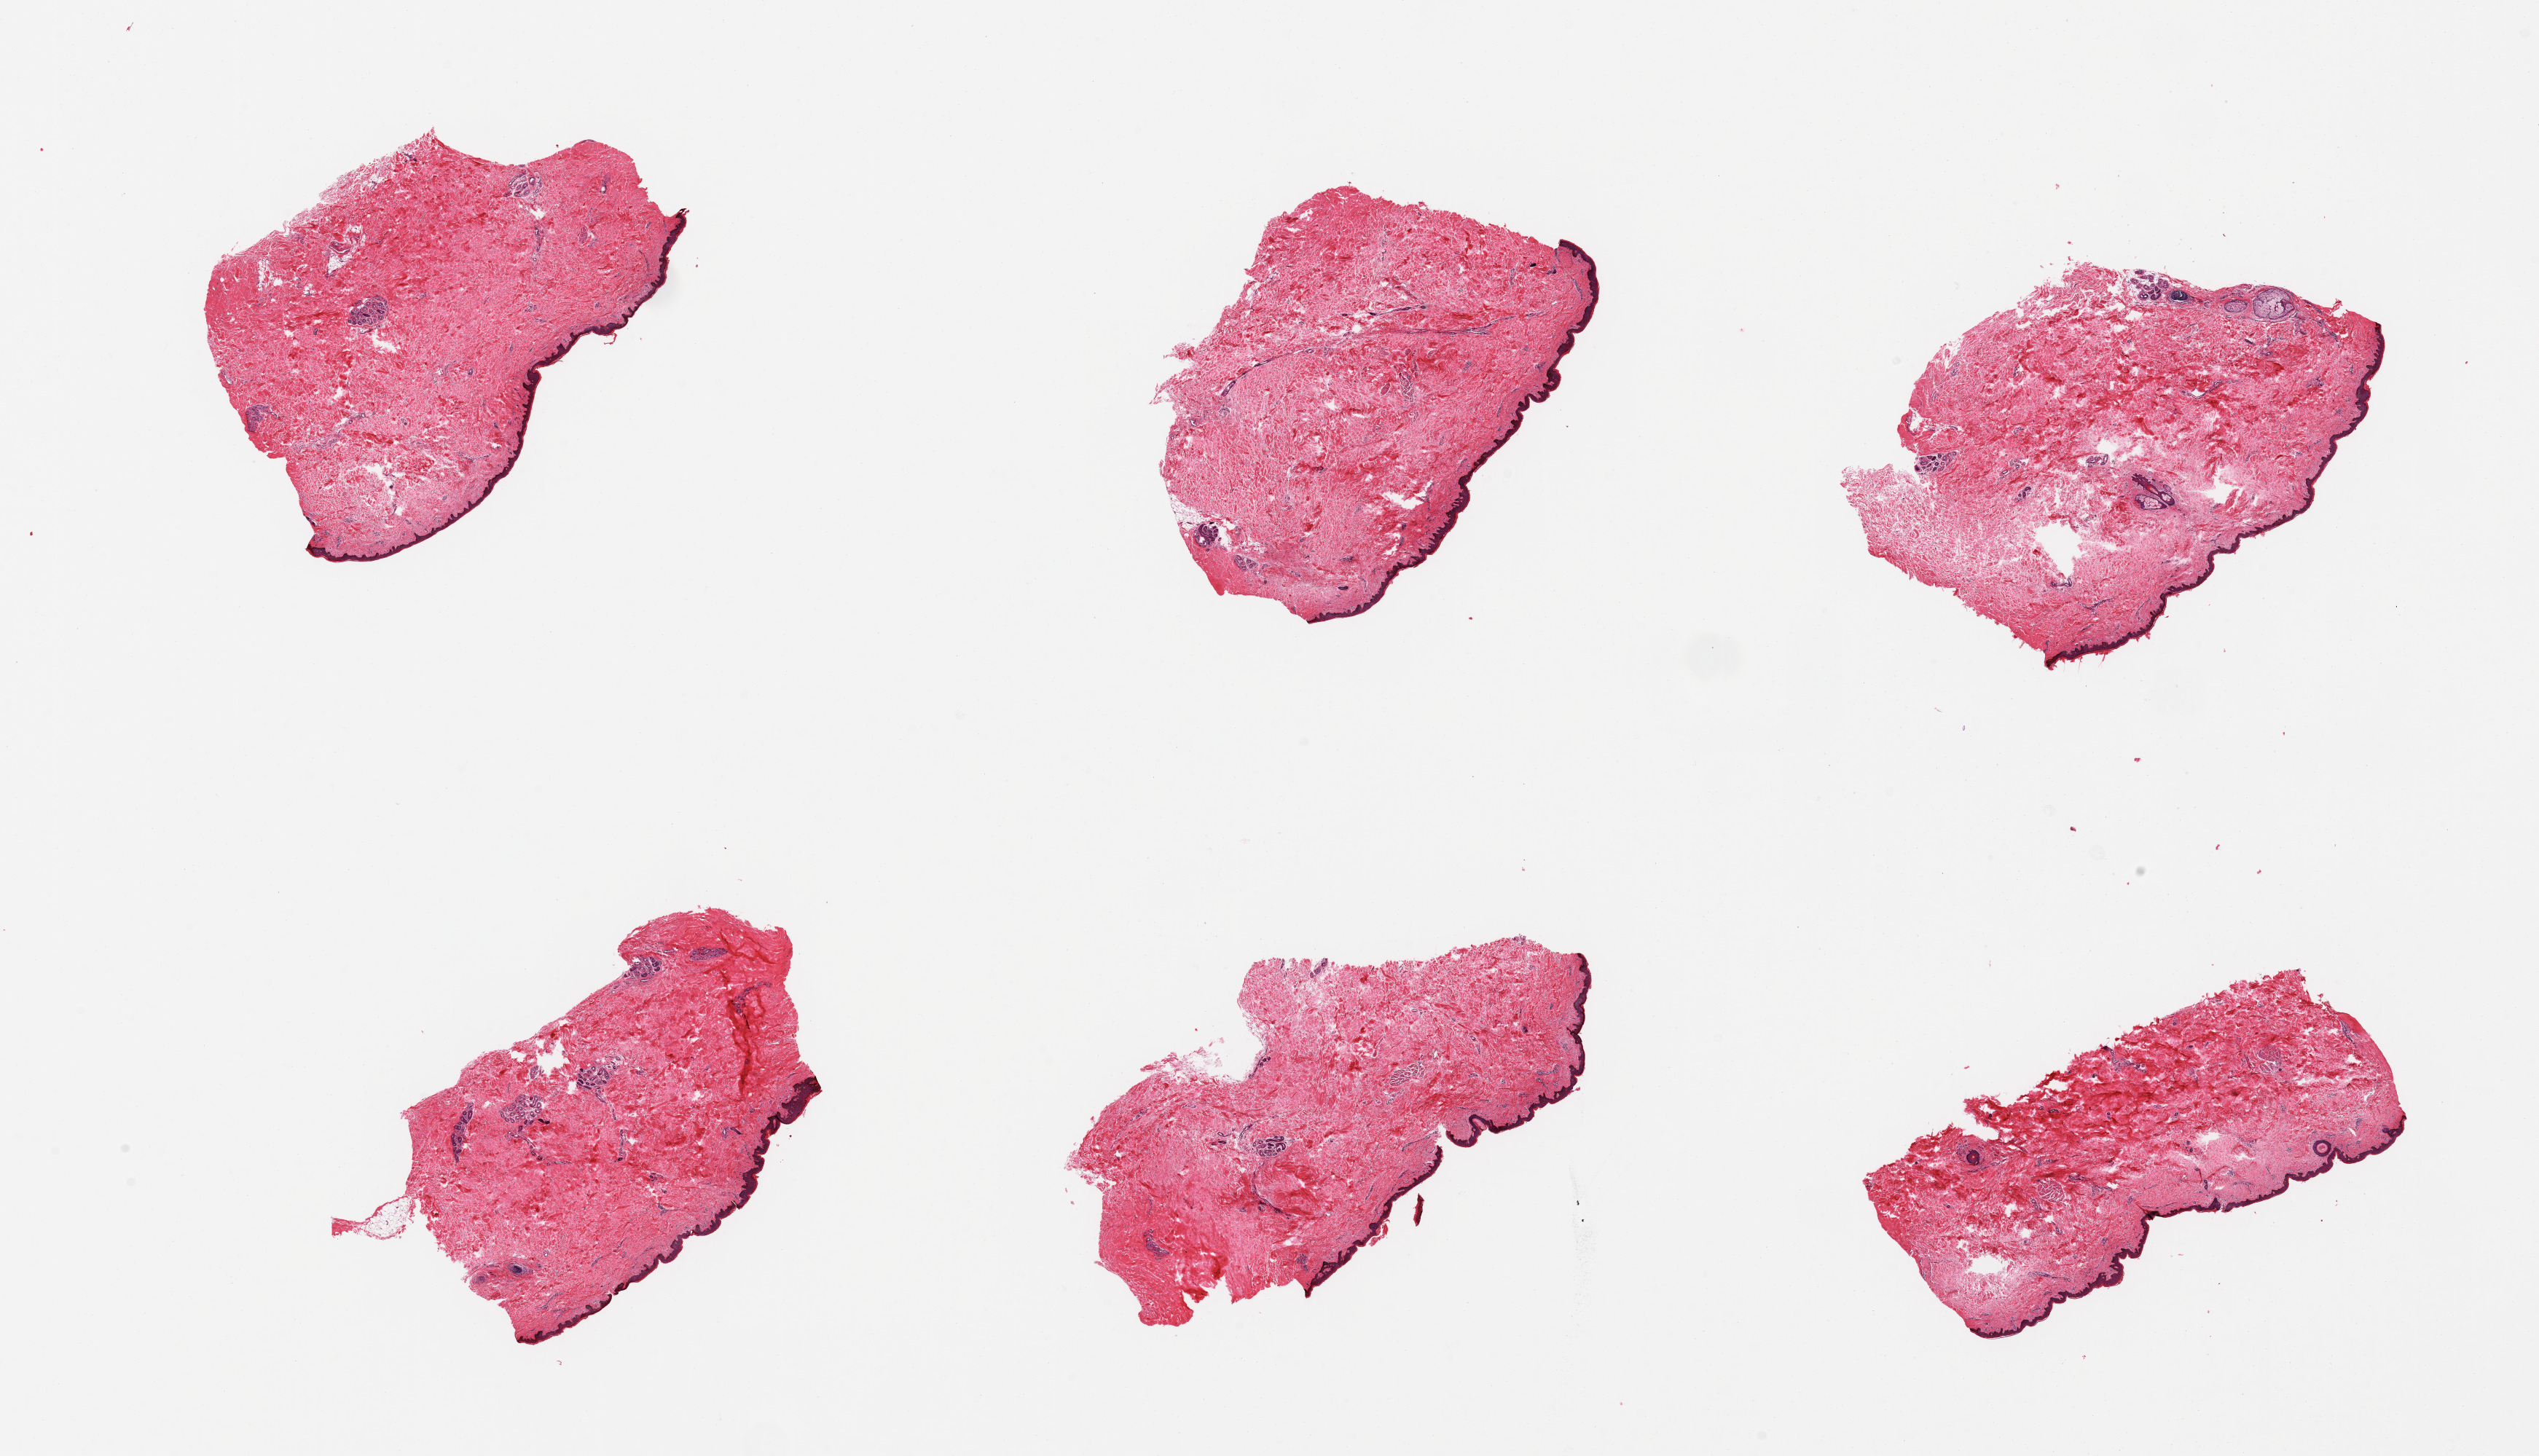
Whole-slide image, hematoxylin and eosin (H&E) stain, a low-resolution overview of the entire scanned area, about 27.6 x 15.8 mm (acquisition: 20x scan), PAXgene-fixed paraffin-embedded (PFPE) section, target tissue: skin of suprapubic region, tissue donor sample. Donor: female.
- pathologist's review note for this sample: 6 pieces; well trimmed